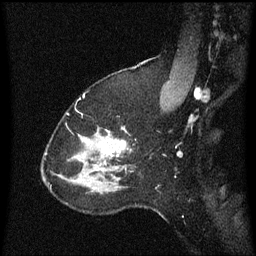
Breast MRI (dynamic contrast-enhanced), one sagittal slice. Slice 46 of 60 in the series (ordered by position). Dynamic contrast-enhanced series, image 2 of 3 at this slice position (ordered by acquisition). 1.5 T. TE 4.2 ms, TR 8.4 ms. 2 mm slice thickness. 256 × 256 image matrix, field of view 200 × 200 mm. Patient: female, 37 years. Case-level facts recorded for this patient, not image findings: setting: breast cancer imaged before/during neoadjuvant chemotherapy; receptor status: HR-positive, HER2-negative.
Structures marked on this image (semi-automatic segmentation, software-assisted and operator-edited):
- analysis volume of interest (the breast-tissue region the enhancement analysis was run in; not a lesion): bounding box <95,126,132,171> (left, top, right, bottom; pixels)
- tumour enhancement mask (voxels above the 70 % enhancement threshold inside the analysis volume of interest): <117,142,127,151>